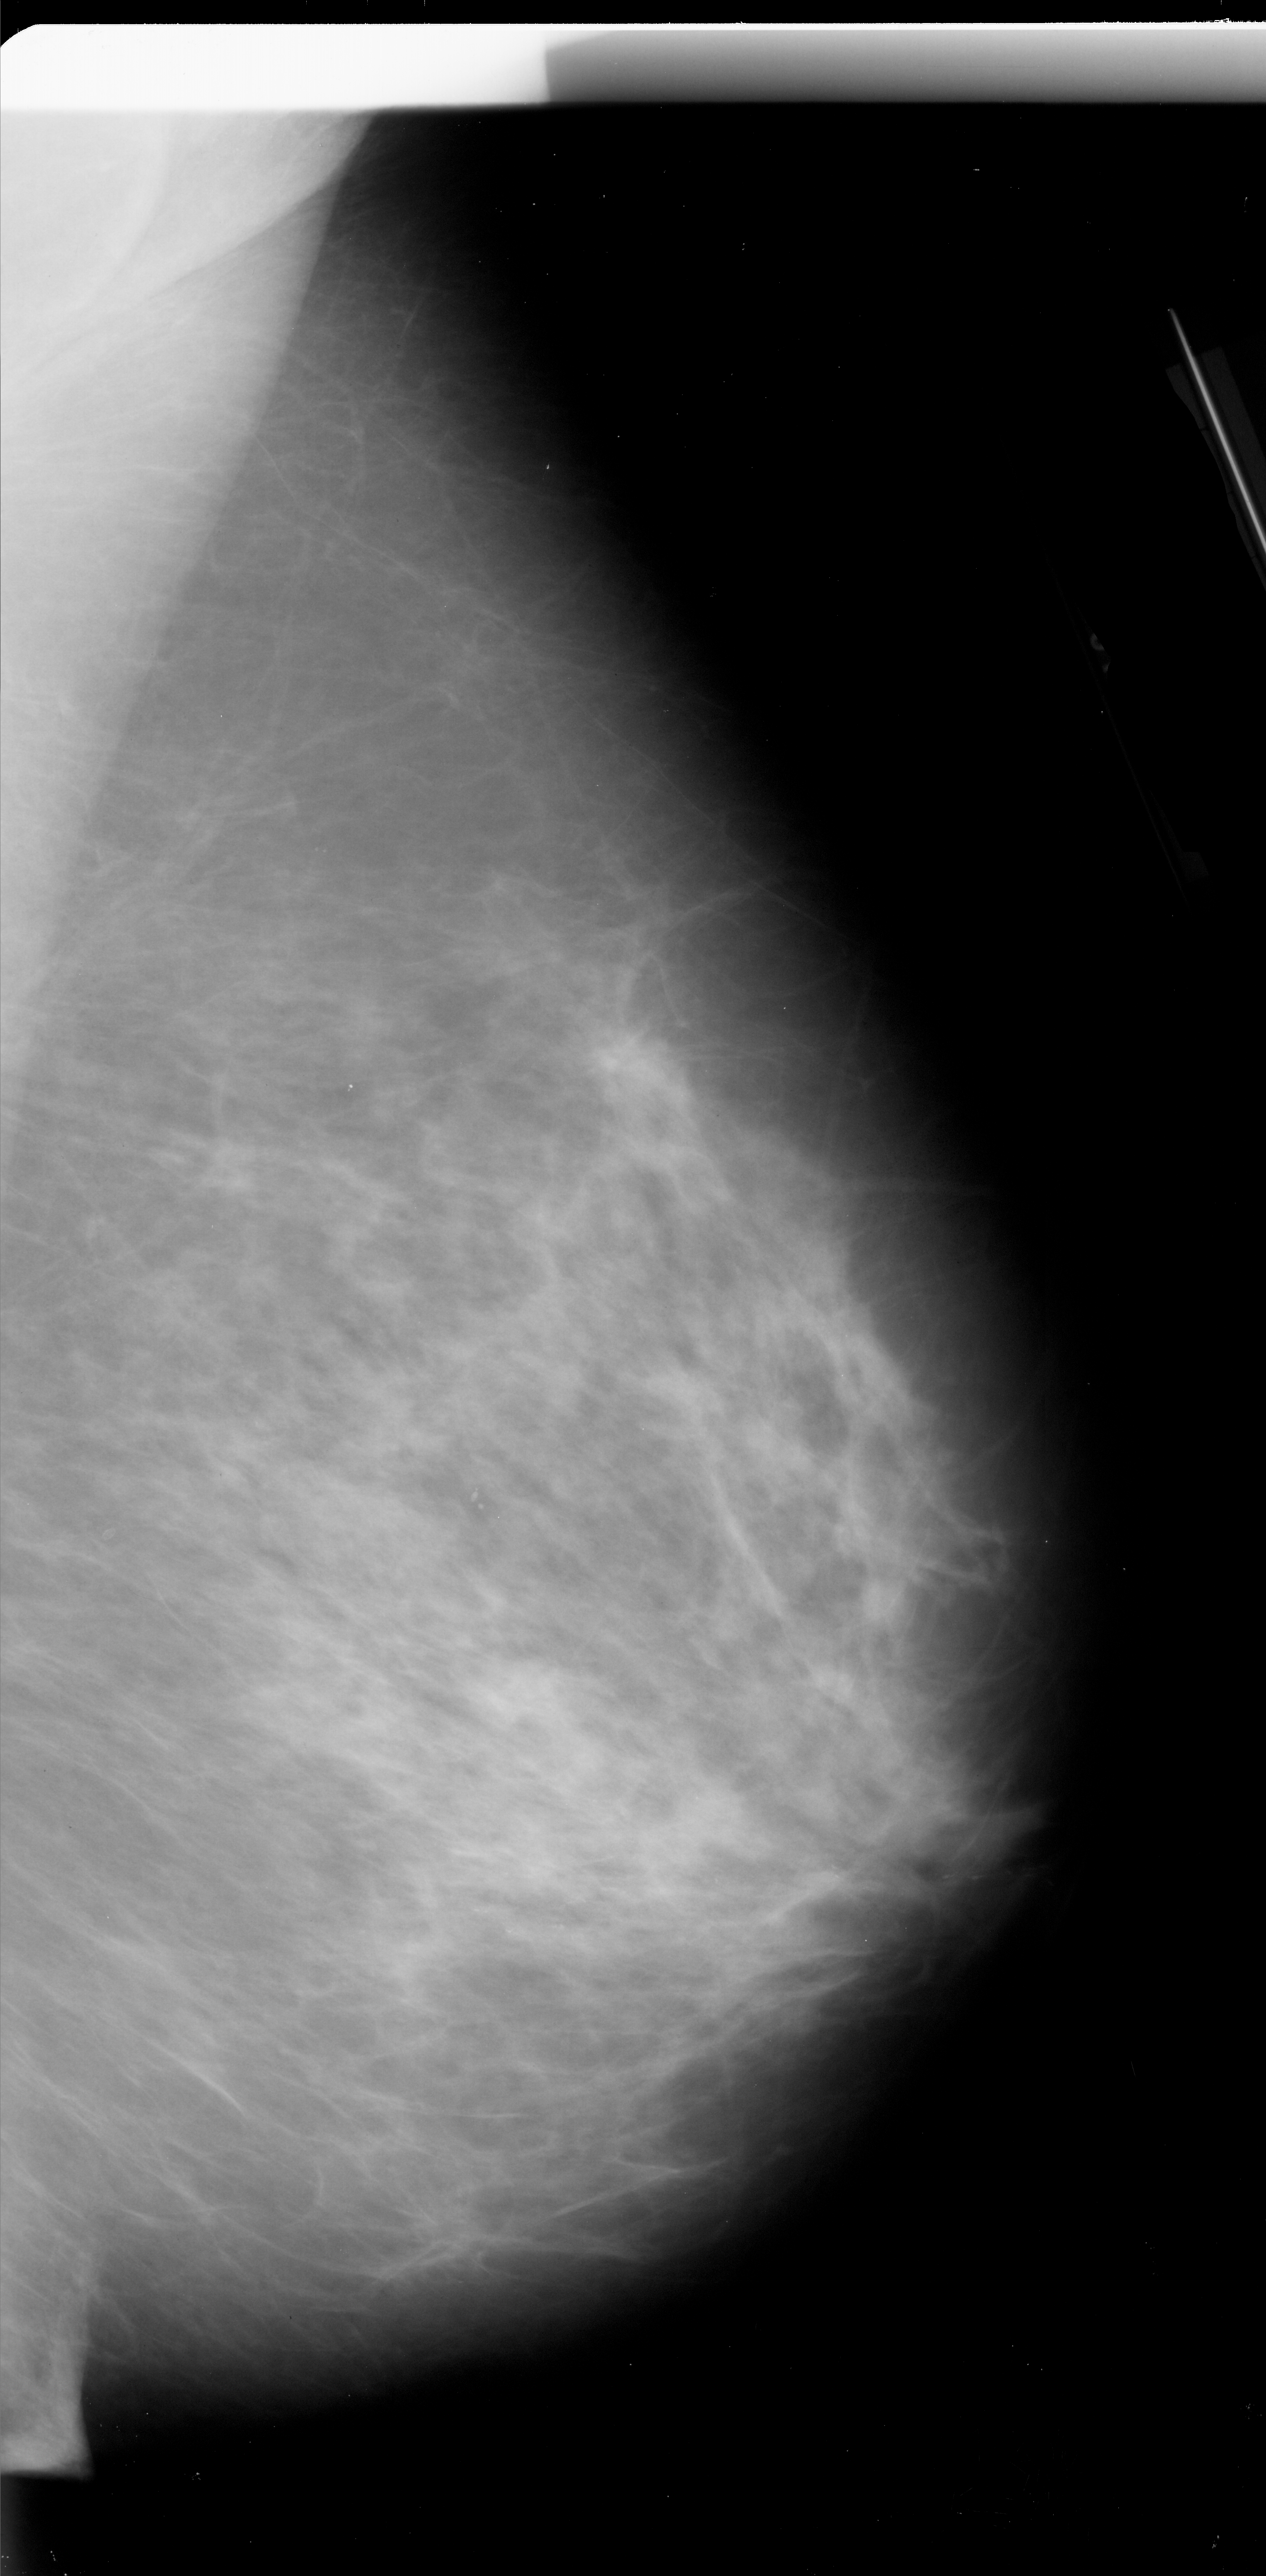
Digitized screen-film mammogram; right breast; mediolateral oblique (MLO) view; BI-RADS breast density category 3 (scale 1–4).
- Marked findings (only marked abnormalities are described; nothing is implied about the rest of the image): calcifications, morphology pleomorphic, distribution linear; BI-RADS assessment category 4; pathology (as recorded): malignant.